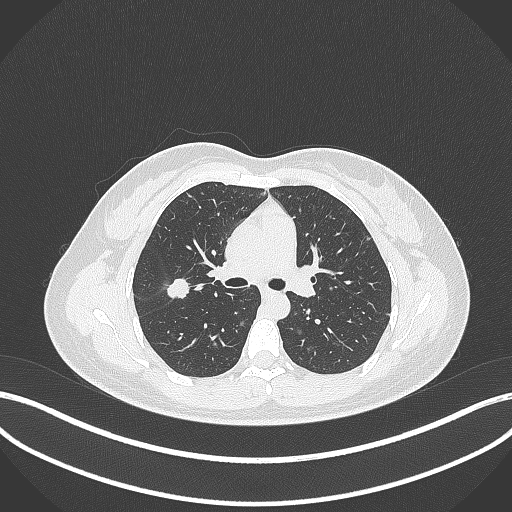
Chest CT, one axial slice; position 208 of 307 along the scan axis; reconstruction kernel B70f; lung window (W 1500 / L -600 HU); 1 mm slice thickness; 512 × 512 image matrix. Patient: female, 33 years. Case-level facts recorded for this patient, not image findings: clinical TNM (as recorded): T1c N0 M0; histopathological grade: G2-G3.
Annotated regions visible in this slice (rectangle marked by the reading radiologist):
- lung tumour (recorded histology: adenocarcinoma): box from (x=165, y=277) to (x=190, y=303) px